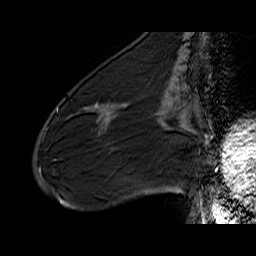
Breast MRI (dynamic contrast-enhanced), one sagittal slice. Position 22 of 60 along the scan axis. Dynamic contrast-enhanced series, time point 2 of 6 at this slice position (early post-contrast). 1.5 T. TE 6.5 ms, TR 32.9 ms. 4 mm slice thickness. 256 × 256 image matrix, field of view 200 × 200 mm. Female patient. From the clinical record (not read from this slice): setting: breast cancer imaged before/during neoadjuvant chemotherapy; receptor status: HER2-positive.
Annotated regions visible in this slice (semi-automatically segmented with operator editing):
- analysis volume of interest (the breast-tissue region the enhancement analysis was run in; not a lesion): bounding box [x1, y1, x2, y2] px = [72, 88, 133, 137]
- tumour enhancement mask (voxels above the 100 % enhancement threshold inside the analysis volume of interest): [86, 109, 103, 129]